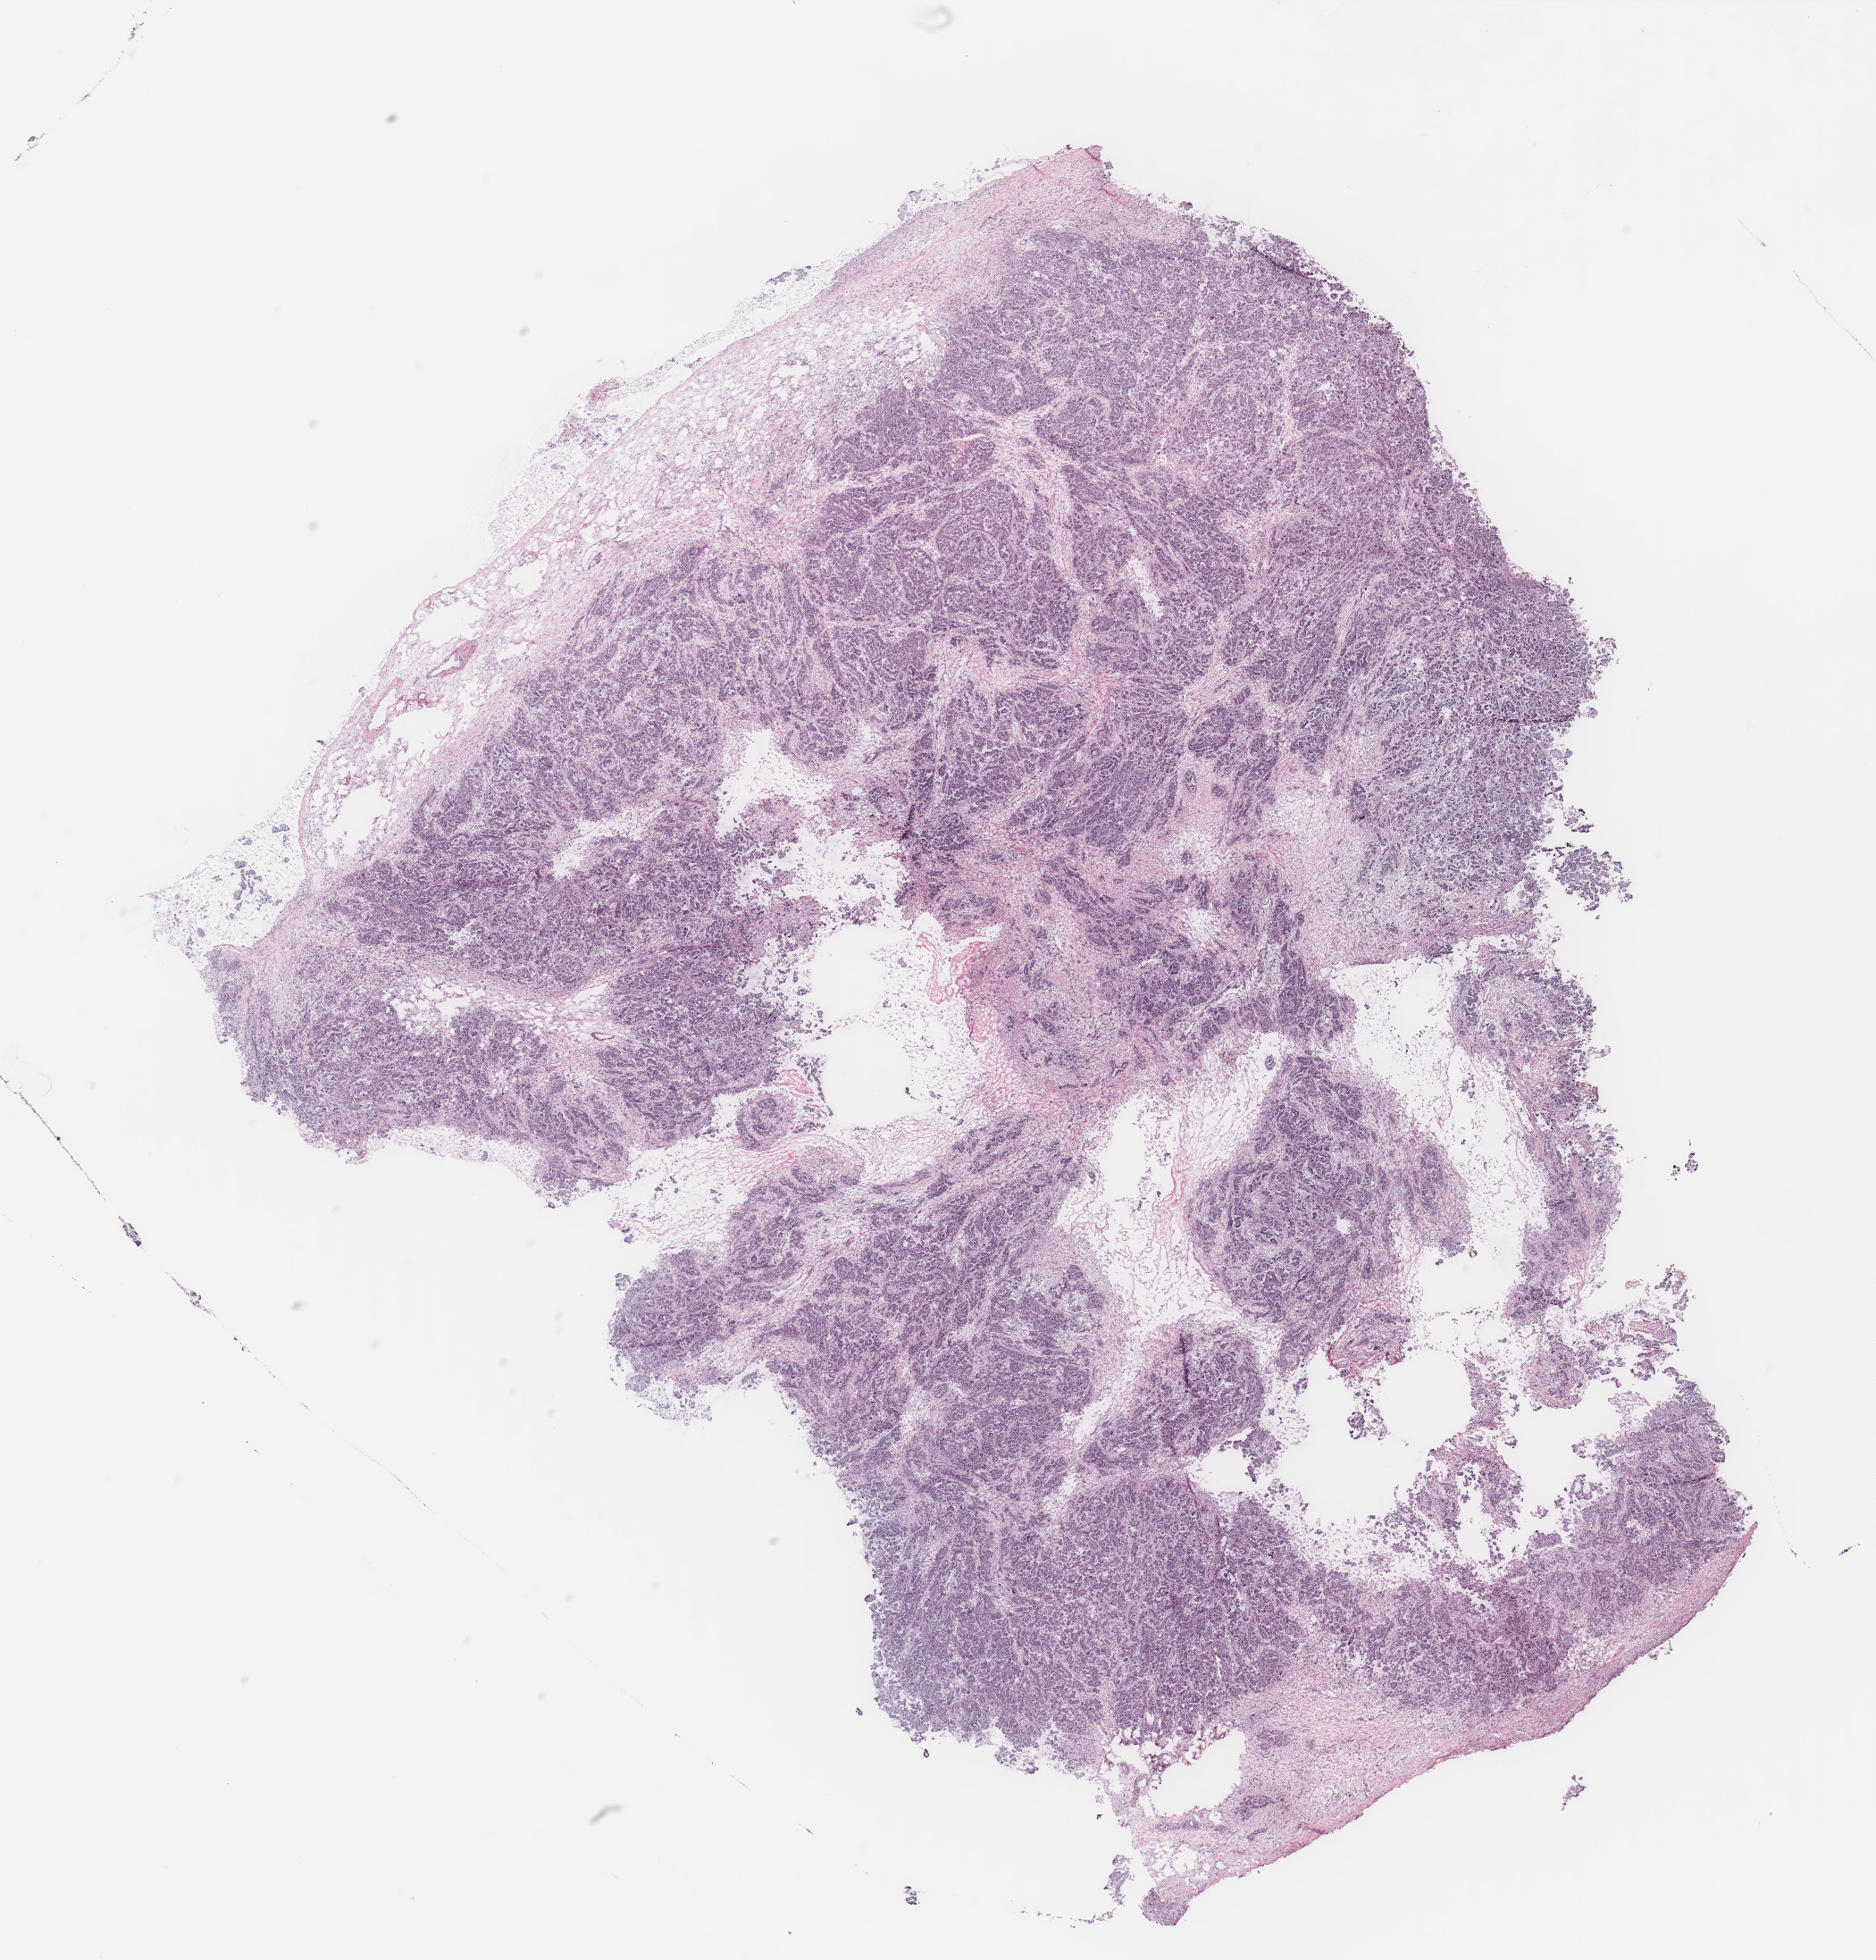
Digitized H&E-stained tissue section (whole slide) — whole scanned area (about 16.8 x 17.6 mm, slide scanned at 40x) shown as a low-resolution overview. Ovary, tumour tissue. Female, 59 y/o.
Histologic diagnosis: Serous adenocarcinoma, NOS.